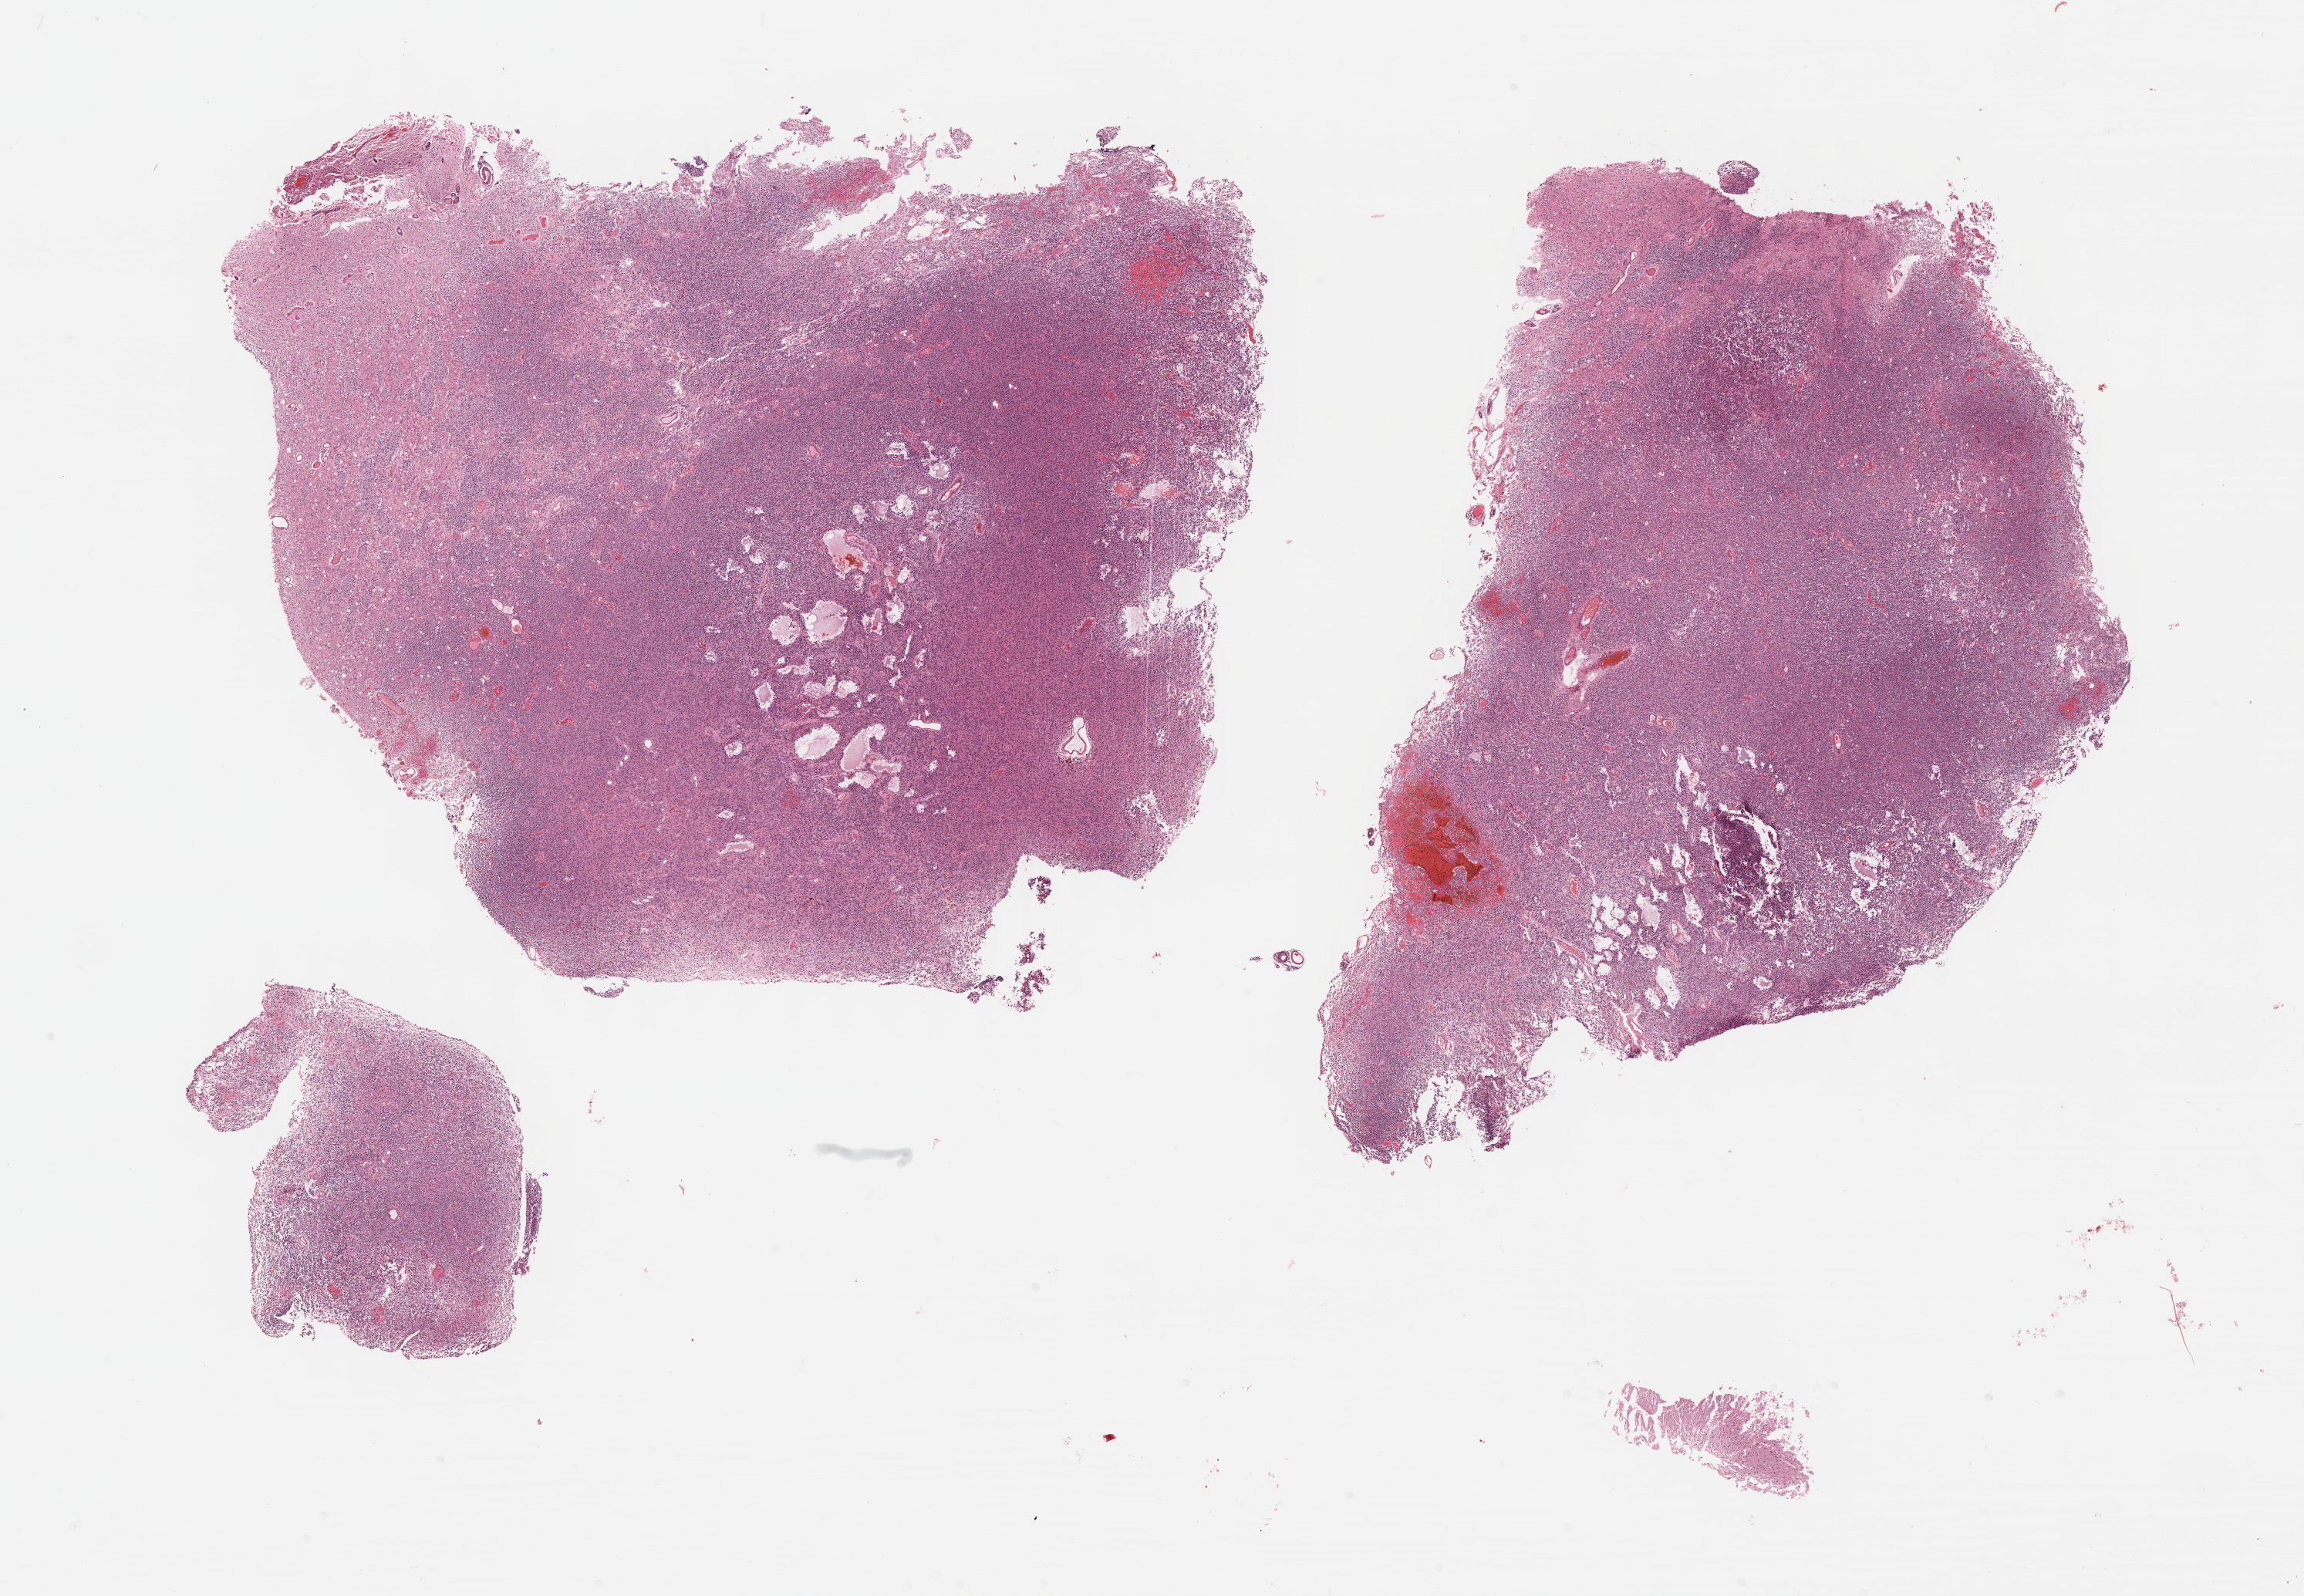
Whole-slide histology image, Hematoxylin and eosin (H&E) stained — shown as a low-resolution overview of the whole scanned area (about 24.2 x 16.7 mm). Formalin-fixed paraffin-embedded (FFPE) diagnostic section. Sample: primary tumour, brain. Male, age 40 years at initial diagnosis. Histologic grade: G3 (poorly differentiated).
Histologic diagnosis: Oligodendroglioma, anaplastic (cerebrum).